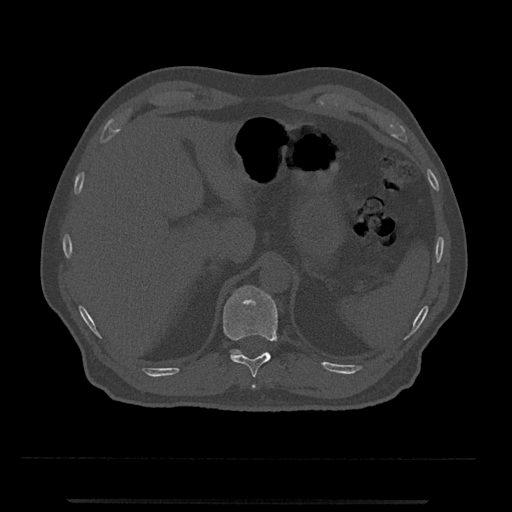
CT including the spine, one axial slice. Slice 454 of 797 in the series (ordered by position). Reconstruction kernel Br40s/3. 120 kVp. Bone window (W 1800 / L 400 HU). 0.5 mm slice thickness. 512 × 512 image matrix, field of view 419 × 419 mm. Male patient, age 63 years. From the clinical record (not read from this slice): primary cancer: prostate.
Annotated regions visible in this slice (semi-automatic segmentation, software-assisted and operator-edited):
- T11 vertebra: bounding box (x1, y1, x2, y2) in pixels: (223, 286, 278, 388)
- T12 vertebra: (230, 349, 242, 358)